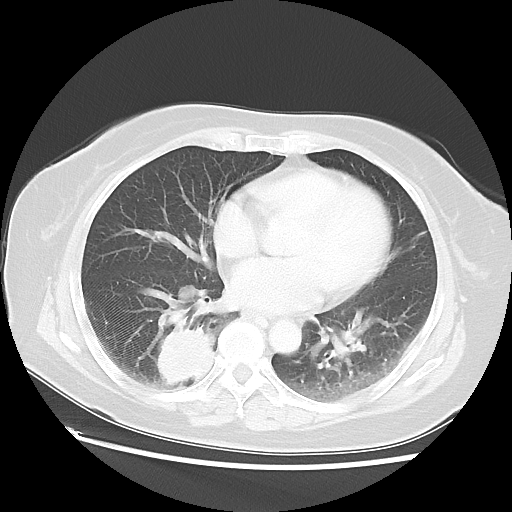
Chest CT, one axial slice. Position 25 of 52 along the scan axis. Lung window (W 1500 / L -600 HU). 5 mm slice thickness. 512 × 512 image matrix, field of view 356 × 356 mm. Patient: female, 69 years. Case-level facts recorded for this patient, not image findings: clinical TNM (as recorded): T2 N1 M1a.
Annotated regions visible in this slice (bounding box drawn by a radiologist):
- lung tumour (recorded histology: adenocarcinoma): bounding box (x1, y1, x2, y2) in pixels: (154, 321, 214, 386)